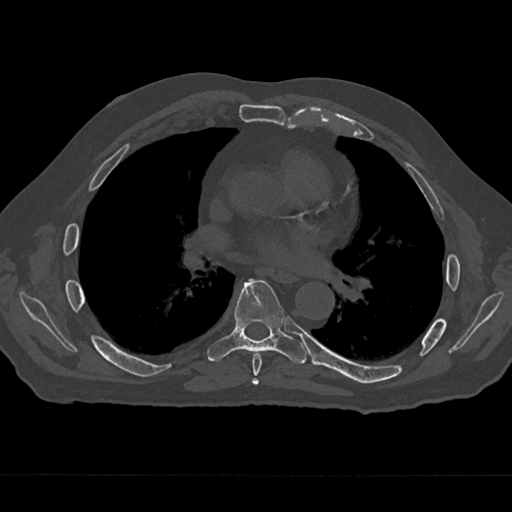
CT including the spine, one axial slice; slice 382 of 797 in the series (ordered by position); bone window (W 1800 / L 400 HU); 0.5 mm slice thickness; 512 × 512 image matrix. Patient: male, 75 years. Case-level facts recorded for this patient, not image findings: primary cancer: renal.
Annotated regions visible in this slice (semi-automatic segmentation, software-assisted and operator-edited):
- T6 vertebra: bounding box [x1, y1, x2, y2] px = [252, 353, 262, 385]
- T7 vertebra: [207, 279, 307, 364]